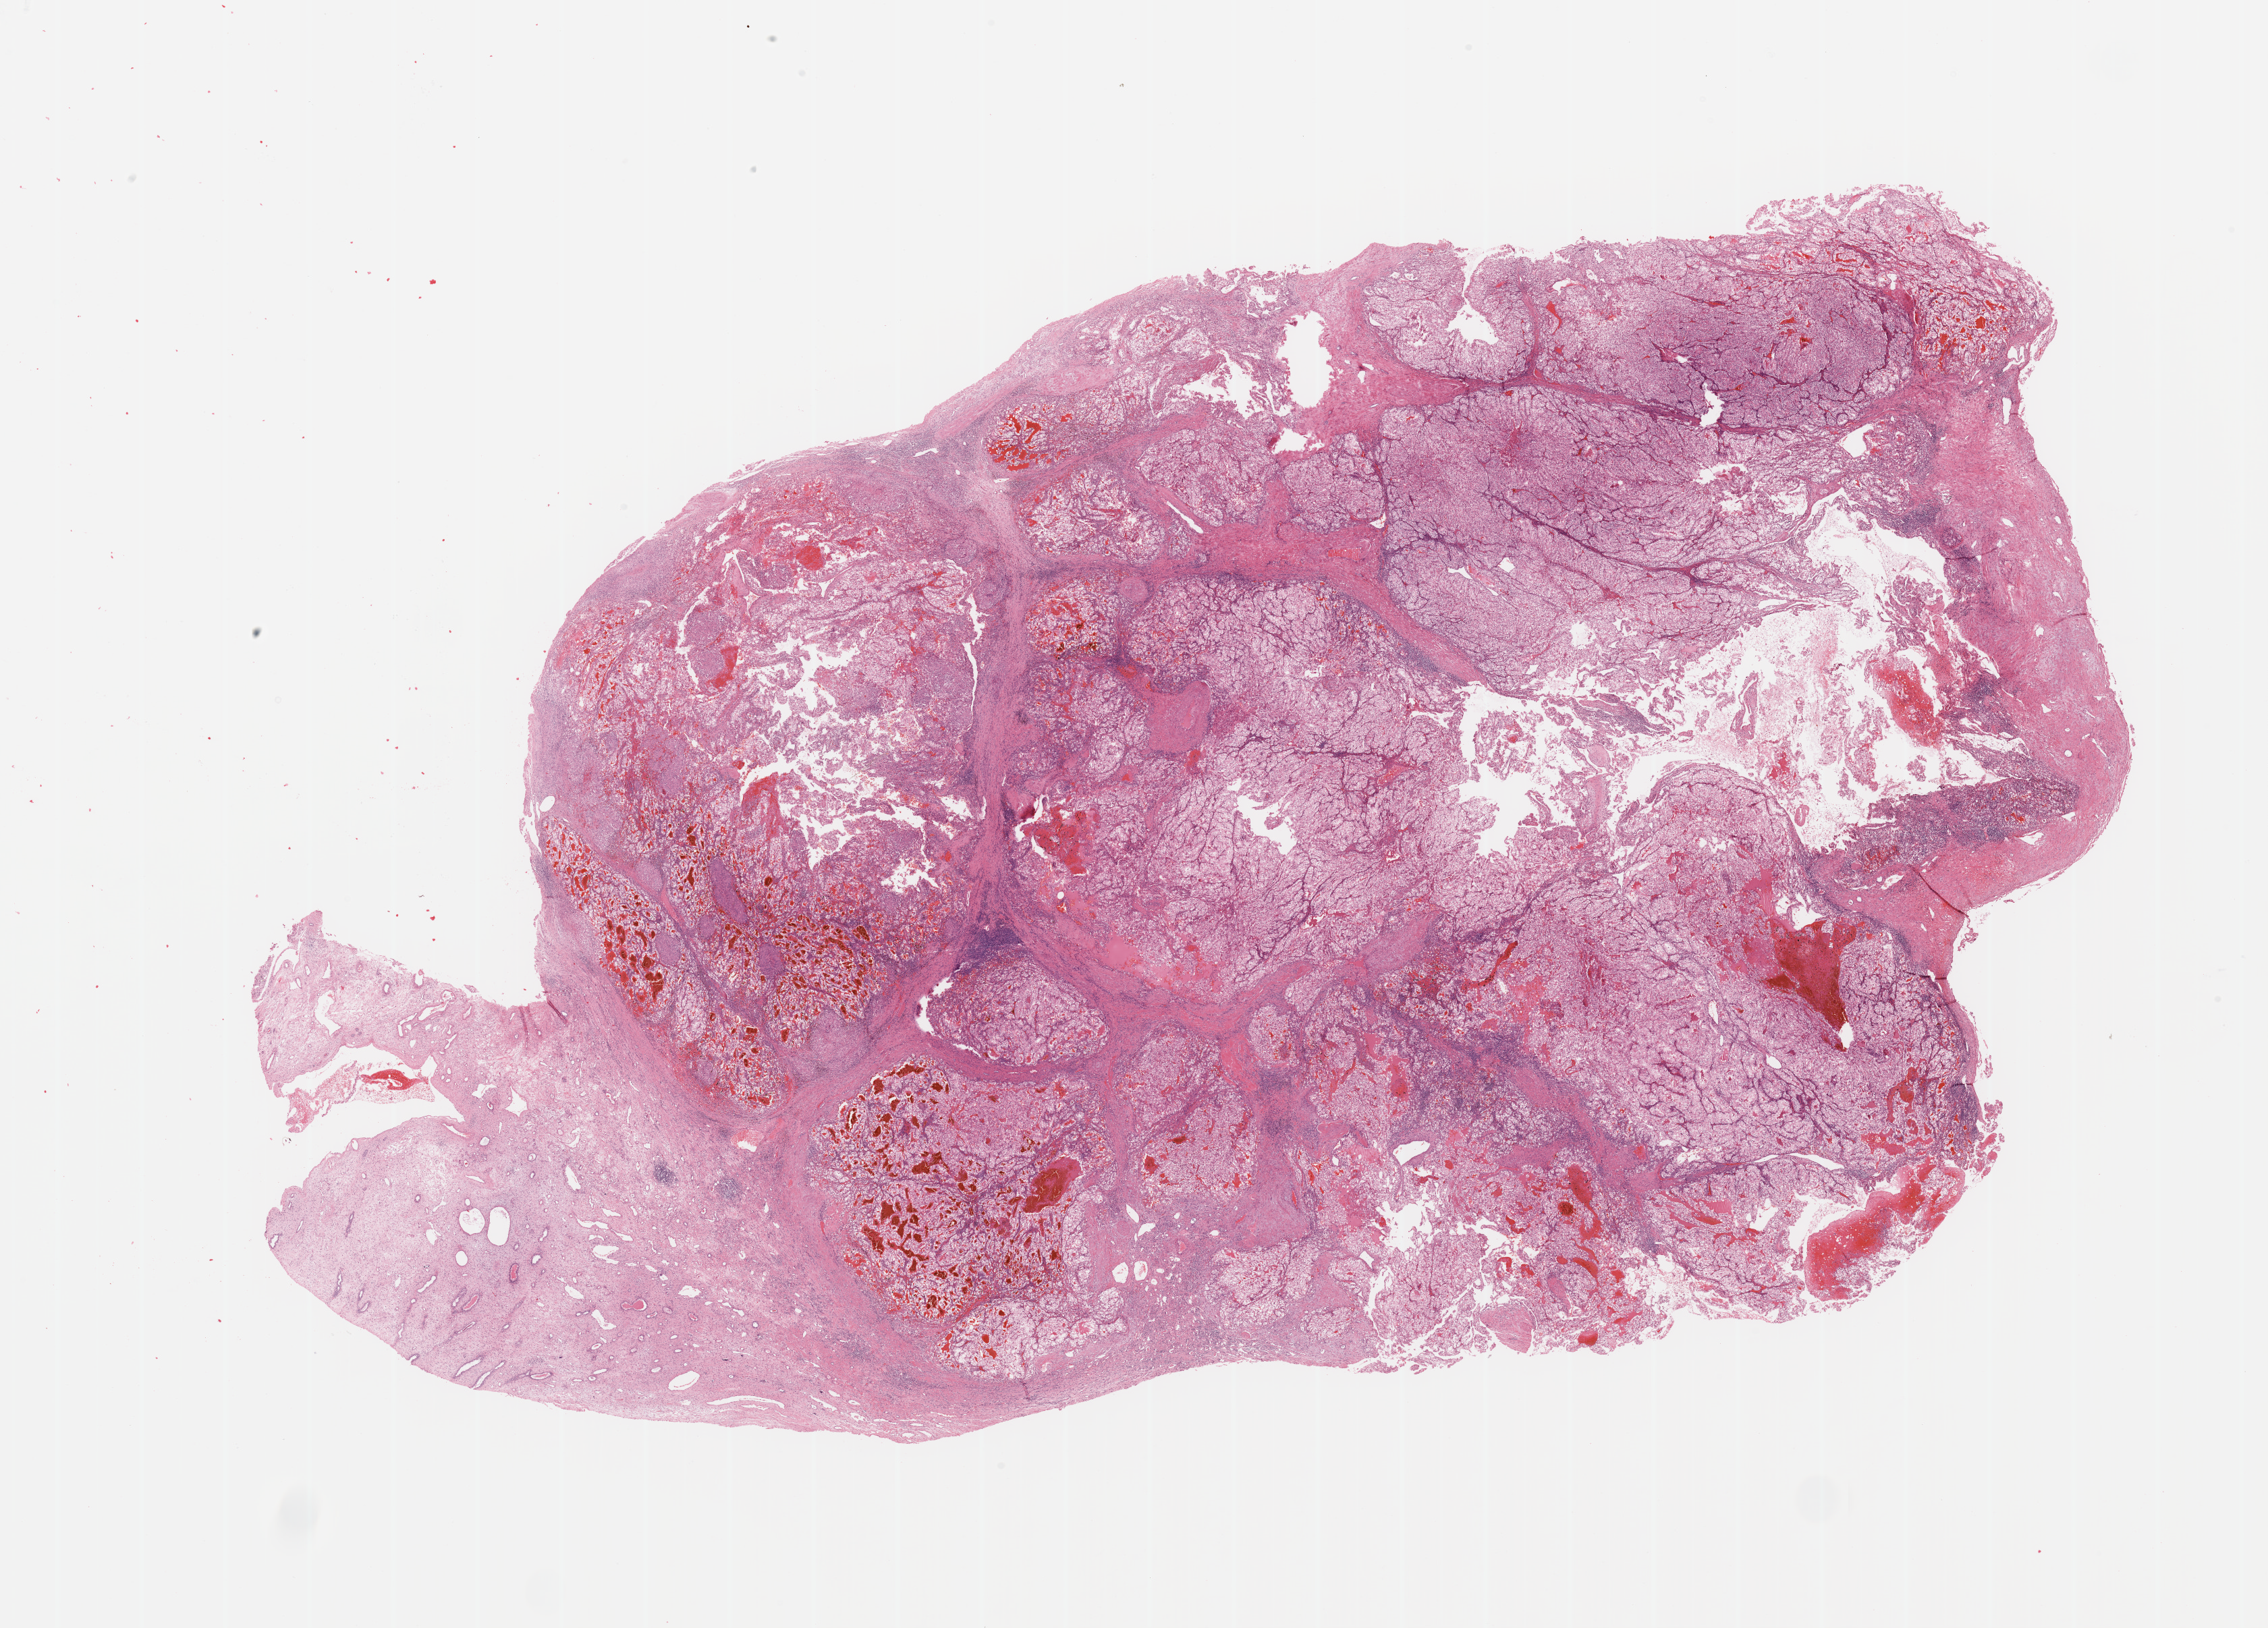
Whole-slide histology image, H&E — a low-resolution overview of the entire scanned area, about 26.6 x 19.1 mm (acquisition: 20x scan); tumour tissue sample, sampled site: kidney. 54-year-old female patient. Histologic grade: G2 (moderately differentiated). Composition of this section per pathologist review: tumour nuclei 80%, necrosis 10%.
- histologic diagnosis: Renal cell carcinoma, NOS